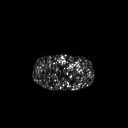
FDG PET of an extremity soft-tissue mass (from a PET/CT study), one axial slice. Position 267 of 267 along the scan axis. 3.27 mm slice thickness. 128 × 128 image matrix, field of view 700 × 700 mm. Patient: male, 63 years. From the clinical record (not read from this slice): histological type: pleiomorphic liposarcoma; grade: high; site of the primary tumour: left thigh.
Structures marked on this image (expert contour drawn on MRI and transferred to this co-registered scan by the dataset authors):
- gross tumour volume including surrounding oedema: bounding box <68,62,80,69> (left, top, right, bottom; pixels)
- gross tumour volume (mass): <68,63,75,69>